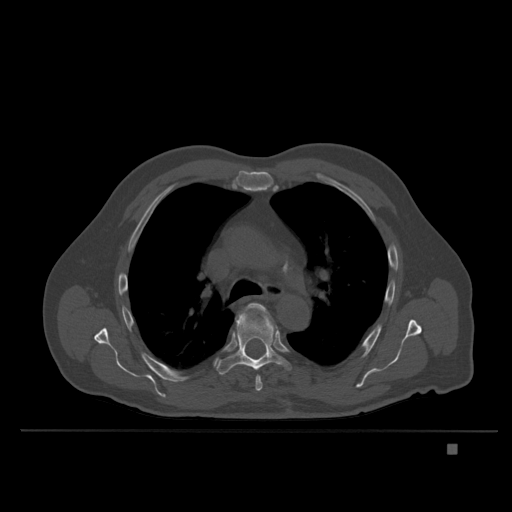
CT including the spine, one axial slice. Position 263 of 435 along the scan axis. Bone window (W 1800 / L 400 HU). 1.5 mm slice thickness. 512 × 512 image matrix. Male patient, age 73 years. Case-level facts recorded for this patient, not image findings: primary cancer: skin.
Annotated regions visible in this slice (semi-automatic segmentation, software-assisted and operator-edited):
- T5 vertebra: bounding box <249,303,264,391> (left, top, right, bottom; pixels)
- T6 vertebra: <215,308,291,376>